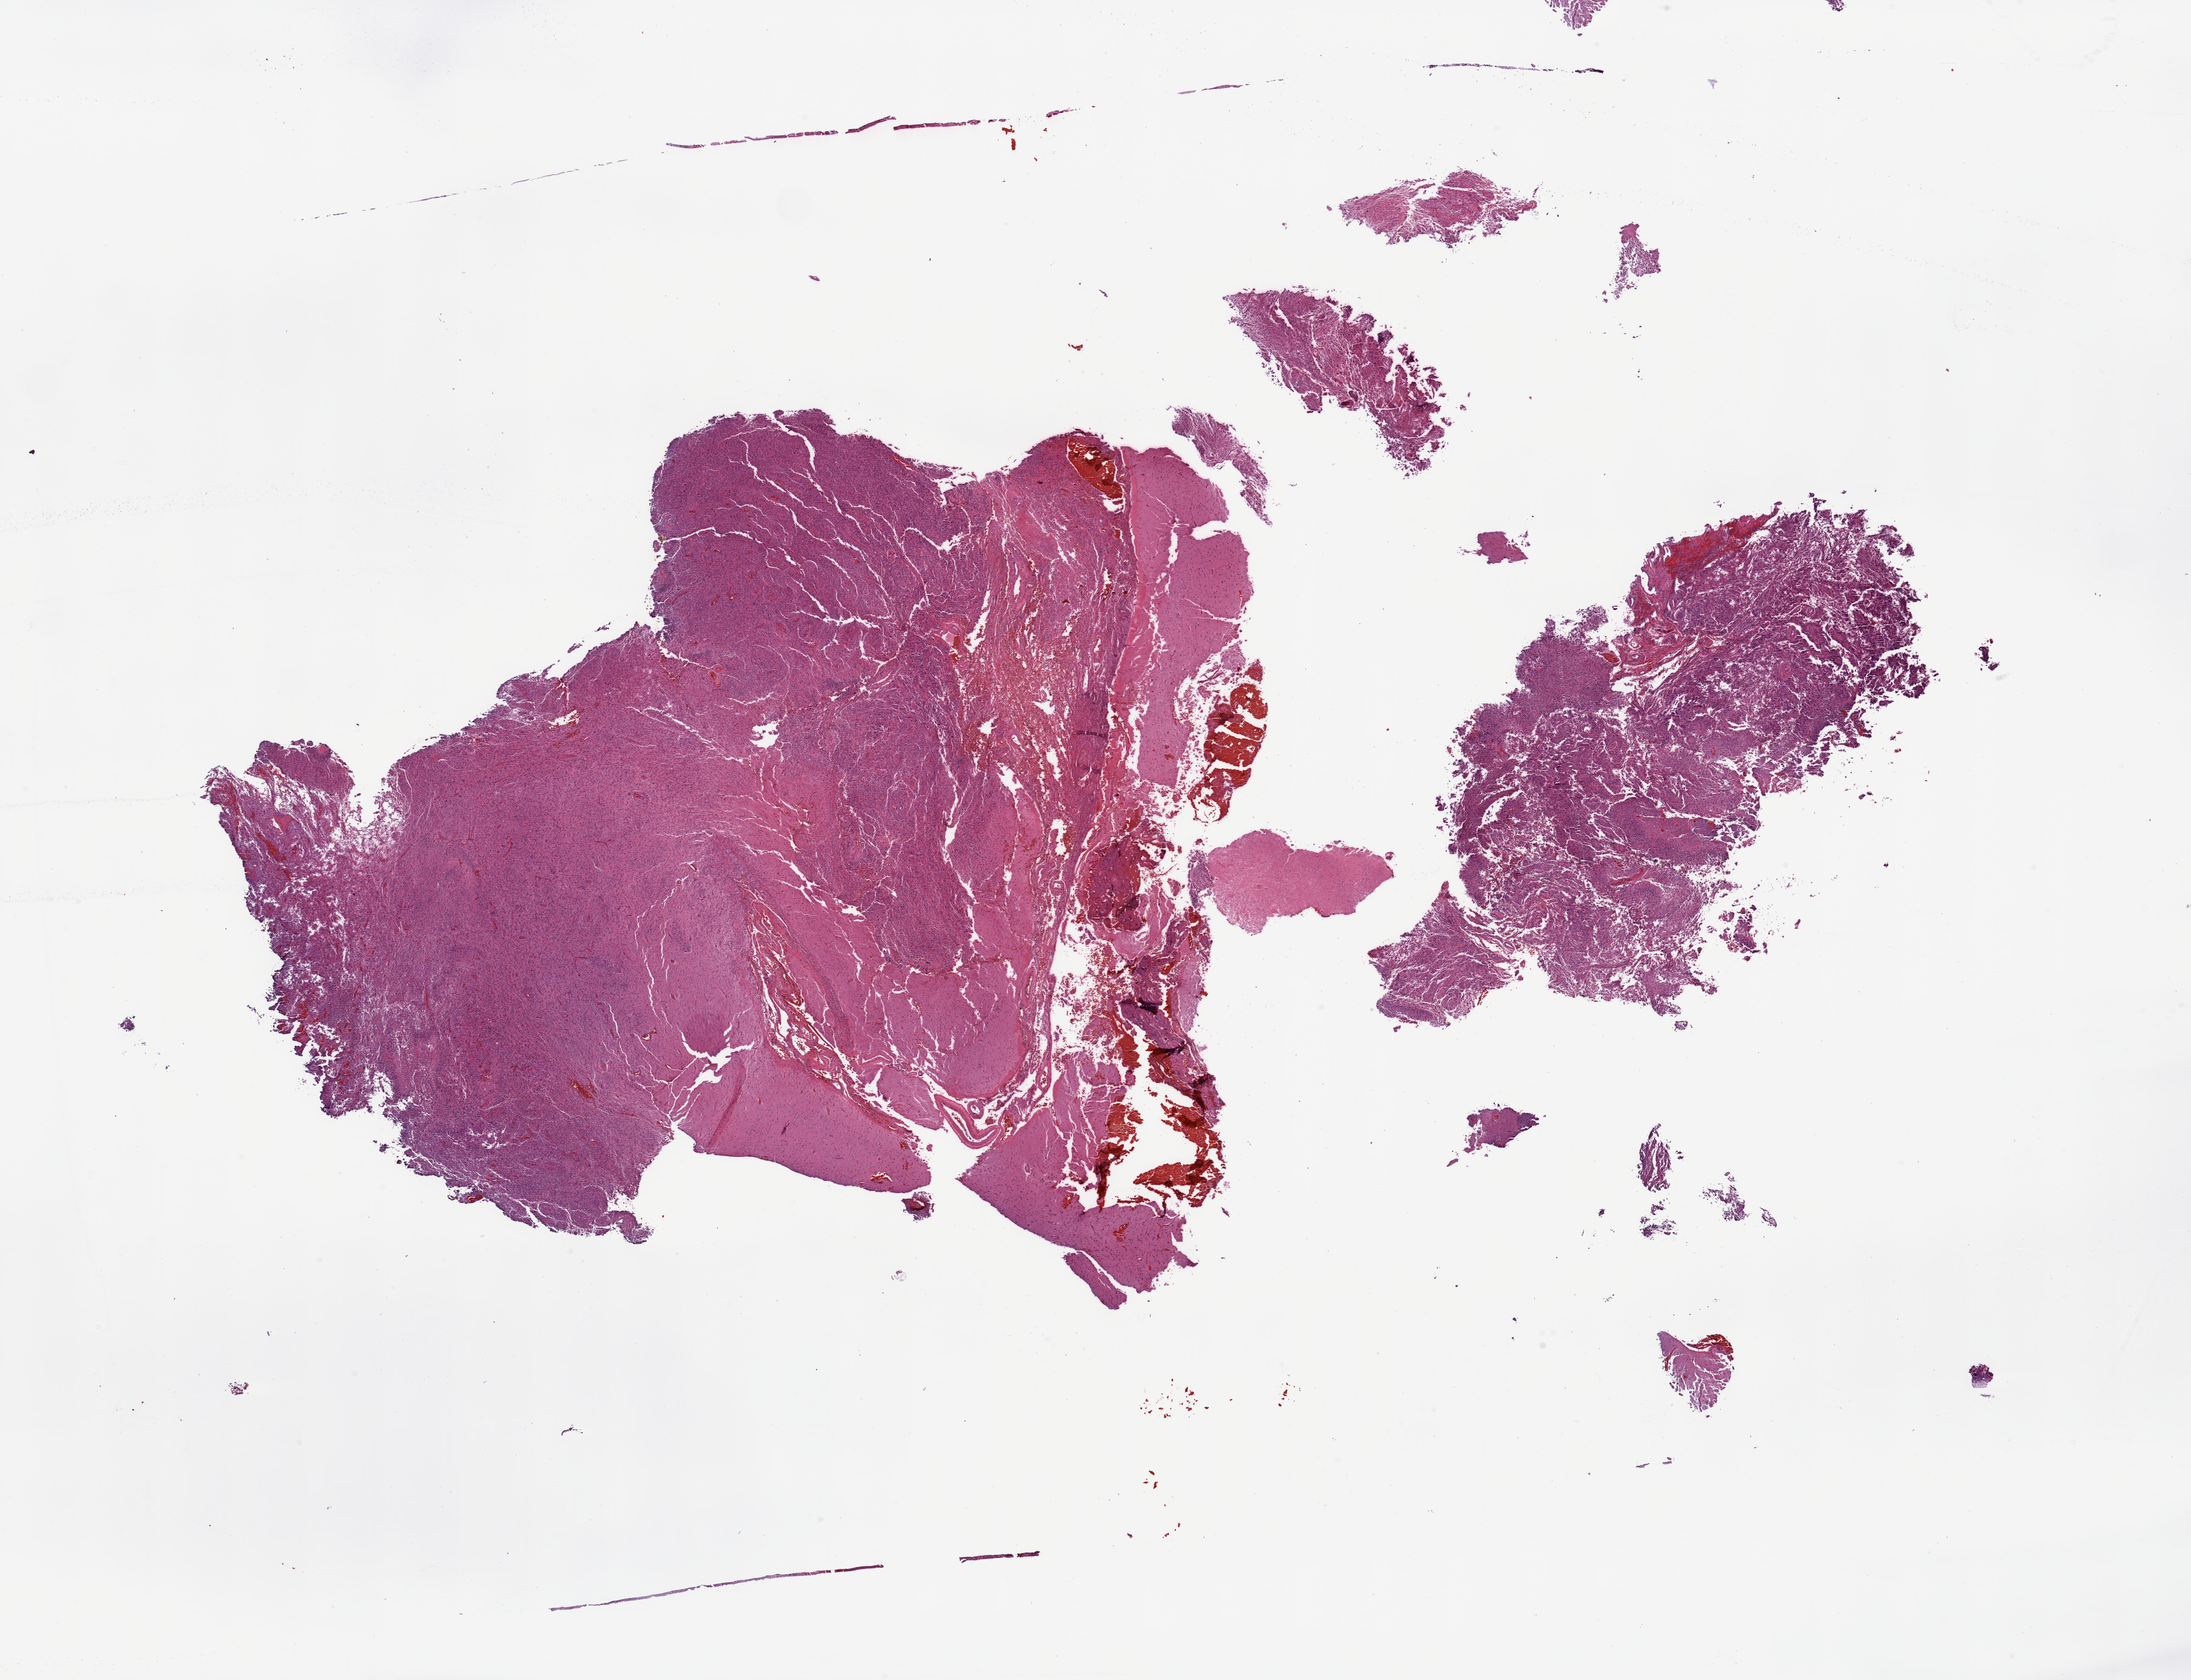
Whole-slide histology image, Hematoxylin and eosin (H&E) stained, low-resolution overview of the scanned area, about 28.5 x 21.9 mm (acquisition: 20x scan), tumour tissue sample, sampled site: brain. Patient: male, age 75 years. Slide review estimates, as recorded: tumour nuclei 75%, necrosis 20%.
Diagnosis: Glioblastoma. Primary tumour site (as recorded): temporal lobe.